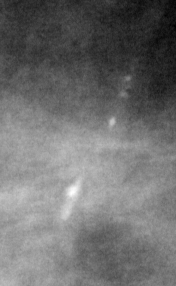
Region of interest cut from a scanned film mammogram (one marked finding), right breast, CC view, BI-RADS breast density category 3 (scale 1–4).
- Finding: calcifications, morphology pleomorphic, distribution linear; BI-RADS assessment category 4; subtlety rating 4 on a 1 (subtle) to 5 (obvious) scale; pathology result (as recorded, not read from the image): malignant.